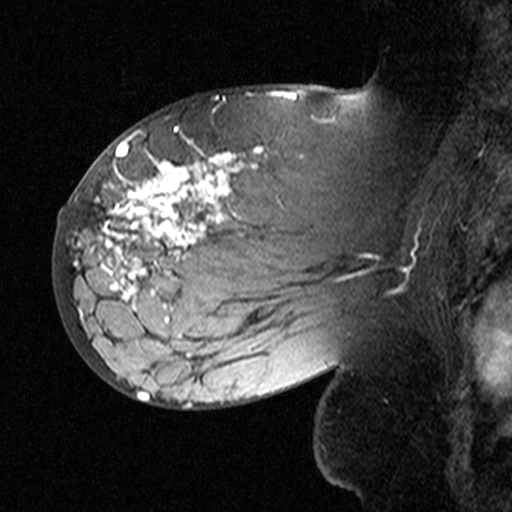
Breast MRI (dynamic contrast-enhanced), one sagittal slice; dynamic contrast-enhanced study with each time point stored as its own series, time point 2 of 3 at this slice position (early post-contrast, ordered by acquisition time); 1.5 T; TE 4.5 ms, TR 11 ms; 3 mm slice thickness; 512 × 512 image matrix, field of view 200 × 200 mm. Female patient, age 53 years. Case-level facts recorded for this patient, not image findings: setting: breast cancer imaged before/during neoadjuvant chemotherapy; receptor status: HR-positive, HER2-negative.
Outlined on this slice (semi-automatic segmentation, software-assisted and operator-edited):
- analysis volume of interest (the breast-tissue region the enhancement analysis was run in; not a lesion): bounding box <76,140,311,353> (left, top, right, bottom; pixels)
- tumour enhancement mask (voxels above the 90 % enhancement threshold inside the analysis volume of interest): <76,147,259,315>